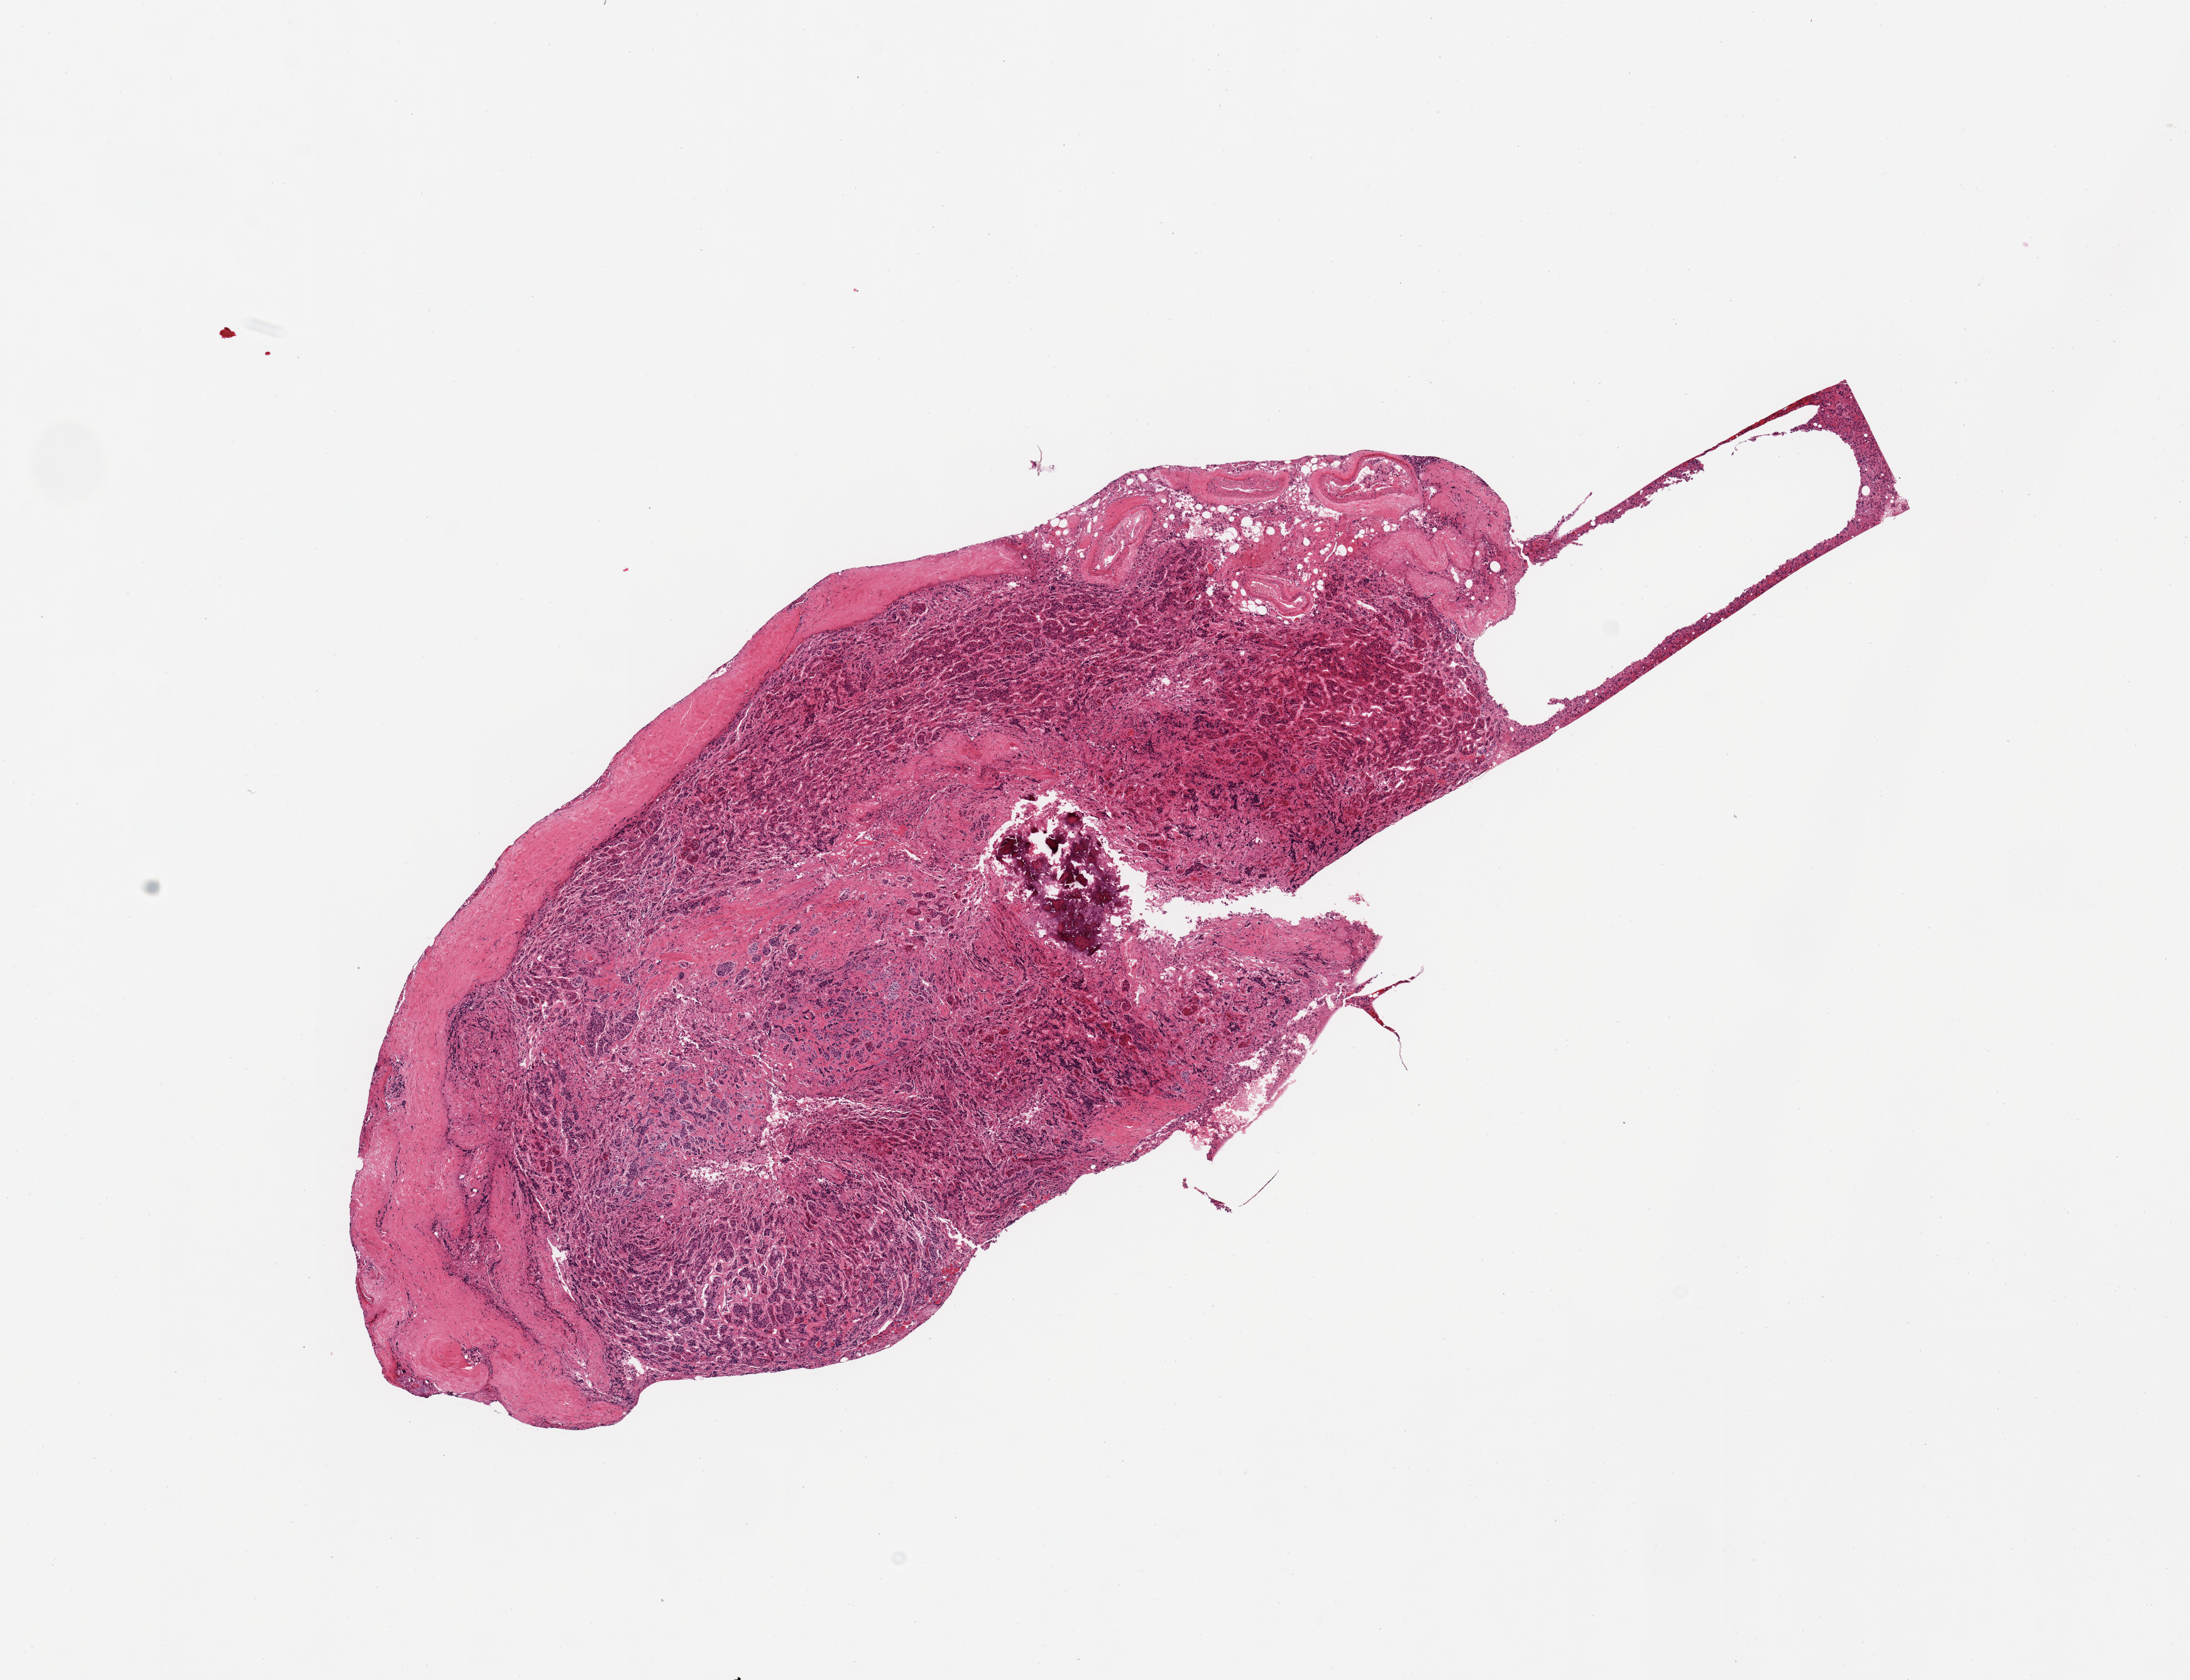
Digitized hematoxylin and eosin (H&E)-stained section, brightfield — a low-resolution overview of the entire scanned area, about 13.8 x 10.6 mm (acquisition: 20x scan), PAXgene-fixed paraffin-embedded (PFPE) section, section of pituitary (target tissue), tissue donor sample. Donor: male.
Pathologist's review note for this sample: 1 piece; moderate autolysis of adenohypophysis; interstitial fibrosis and focal calcification, rim of dense fibrous tissue with vessels consistent with dura mater.